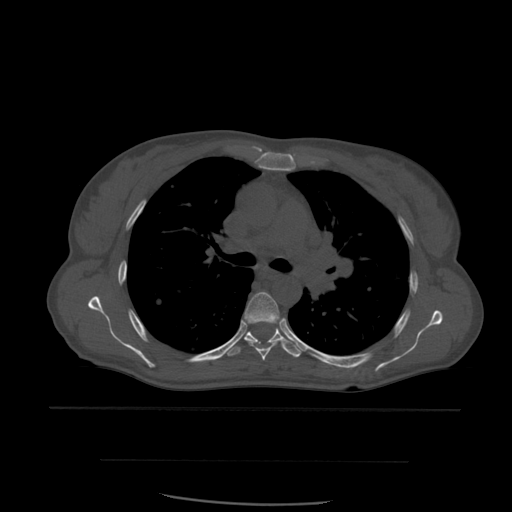
CT including the spine, one axial slice. Position 402 of 574 along the scan axis. Bone window (W 1800 / L 400 HU). 1.25 mm slice thickness. 512 × 512 image matrix, field of view 392 × 392 mm. Patient age 48 years. Case-level facts recorded for this patient, not image findings: primary cancer: lung.
Structures marked on this image (semi-automatically segmented with operator editing):
- T5 vertebra: bounding box [x1, y1, x2, y2] px = [244, 292, 283, 361]
- T6 vertebra: [224, 331, 302, 358]